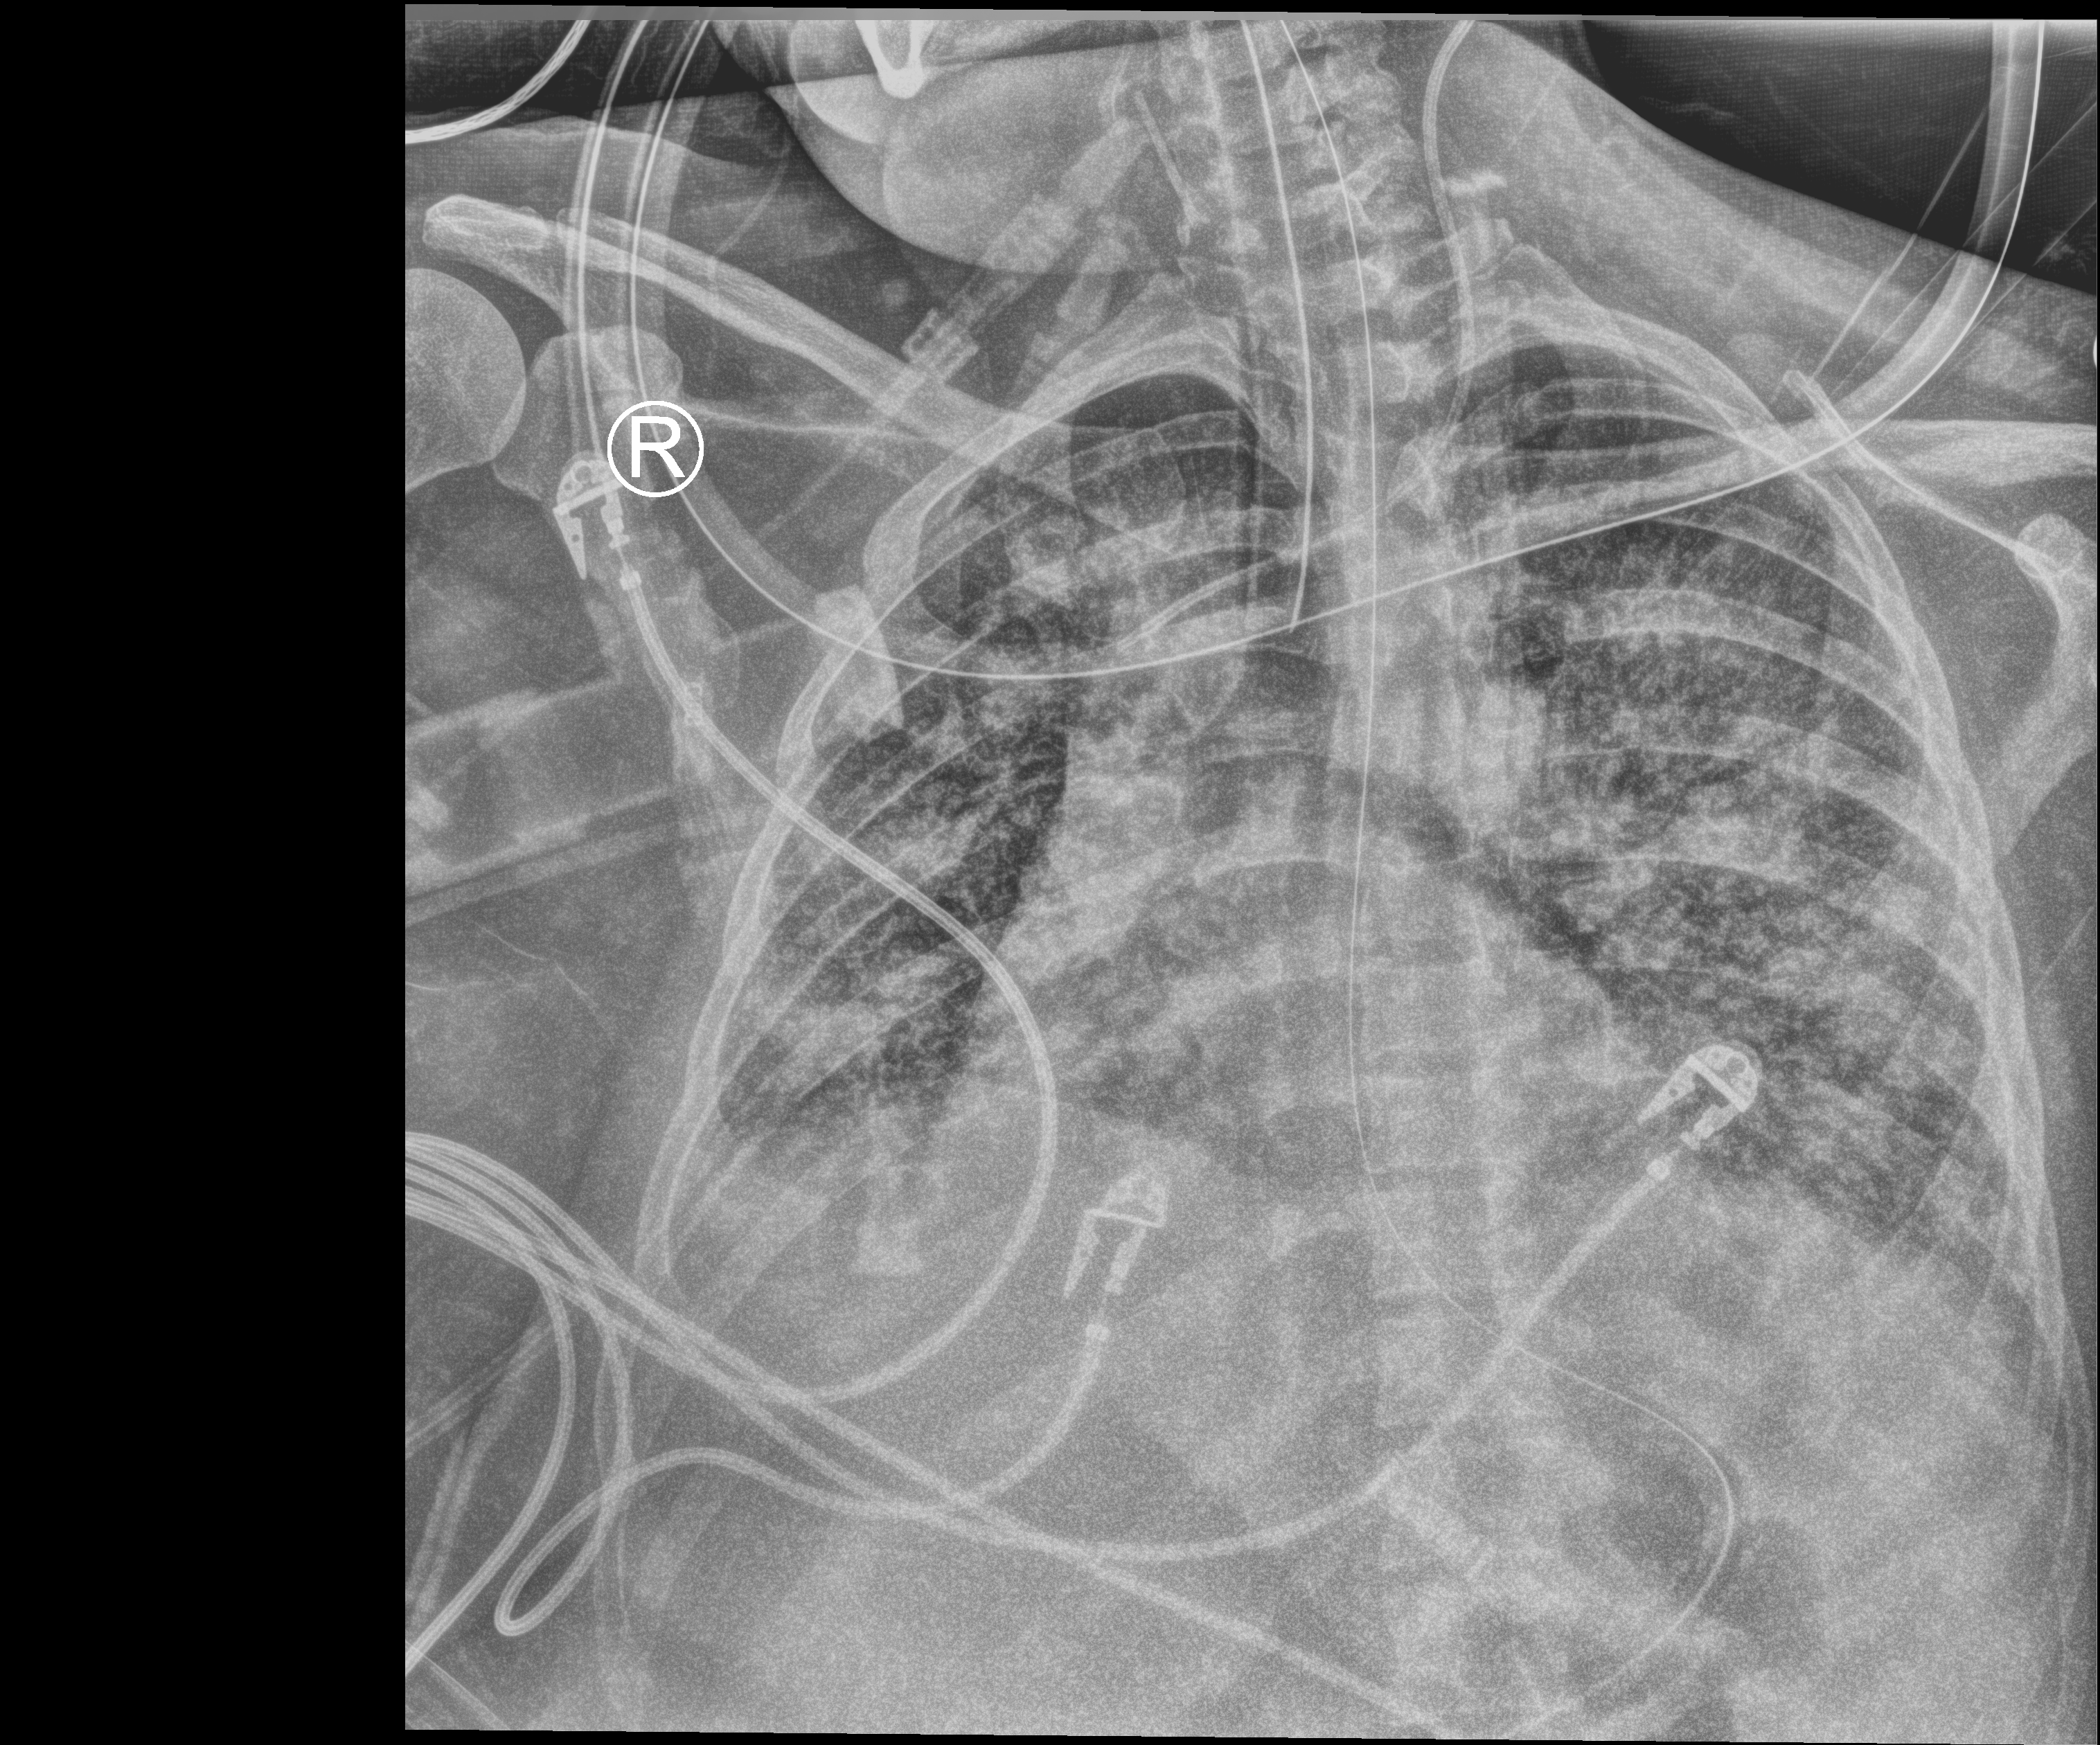
Portable chest radiograph; anteroposterior (AP) projection. Female patient hospitalised with COVID-19, age 18–59 years.
Admission-level facts for this patient (not findings on this image; timing relative to this image not recorded):
- admitted to intensive care during this hospital stay: no